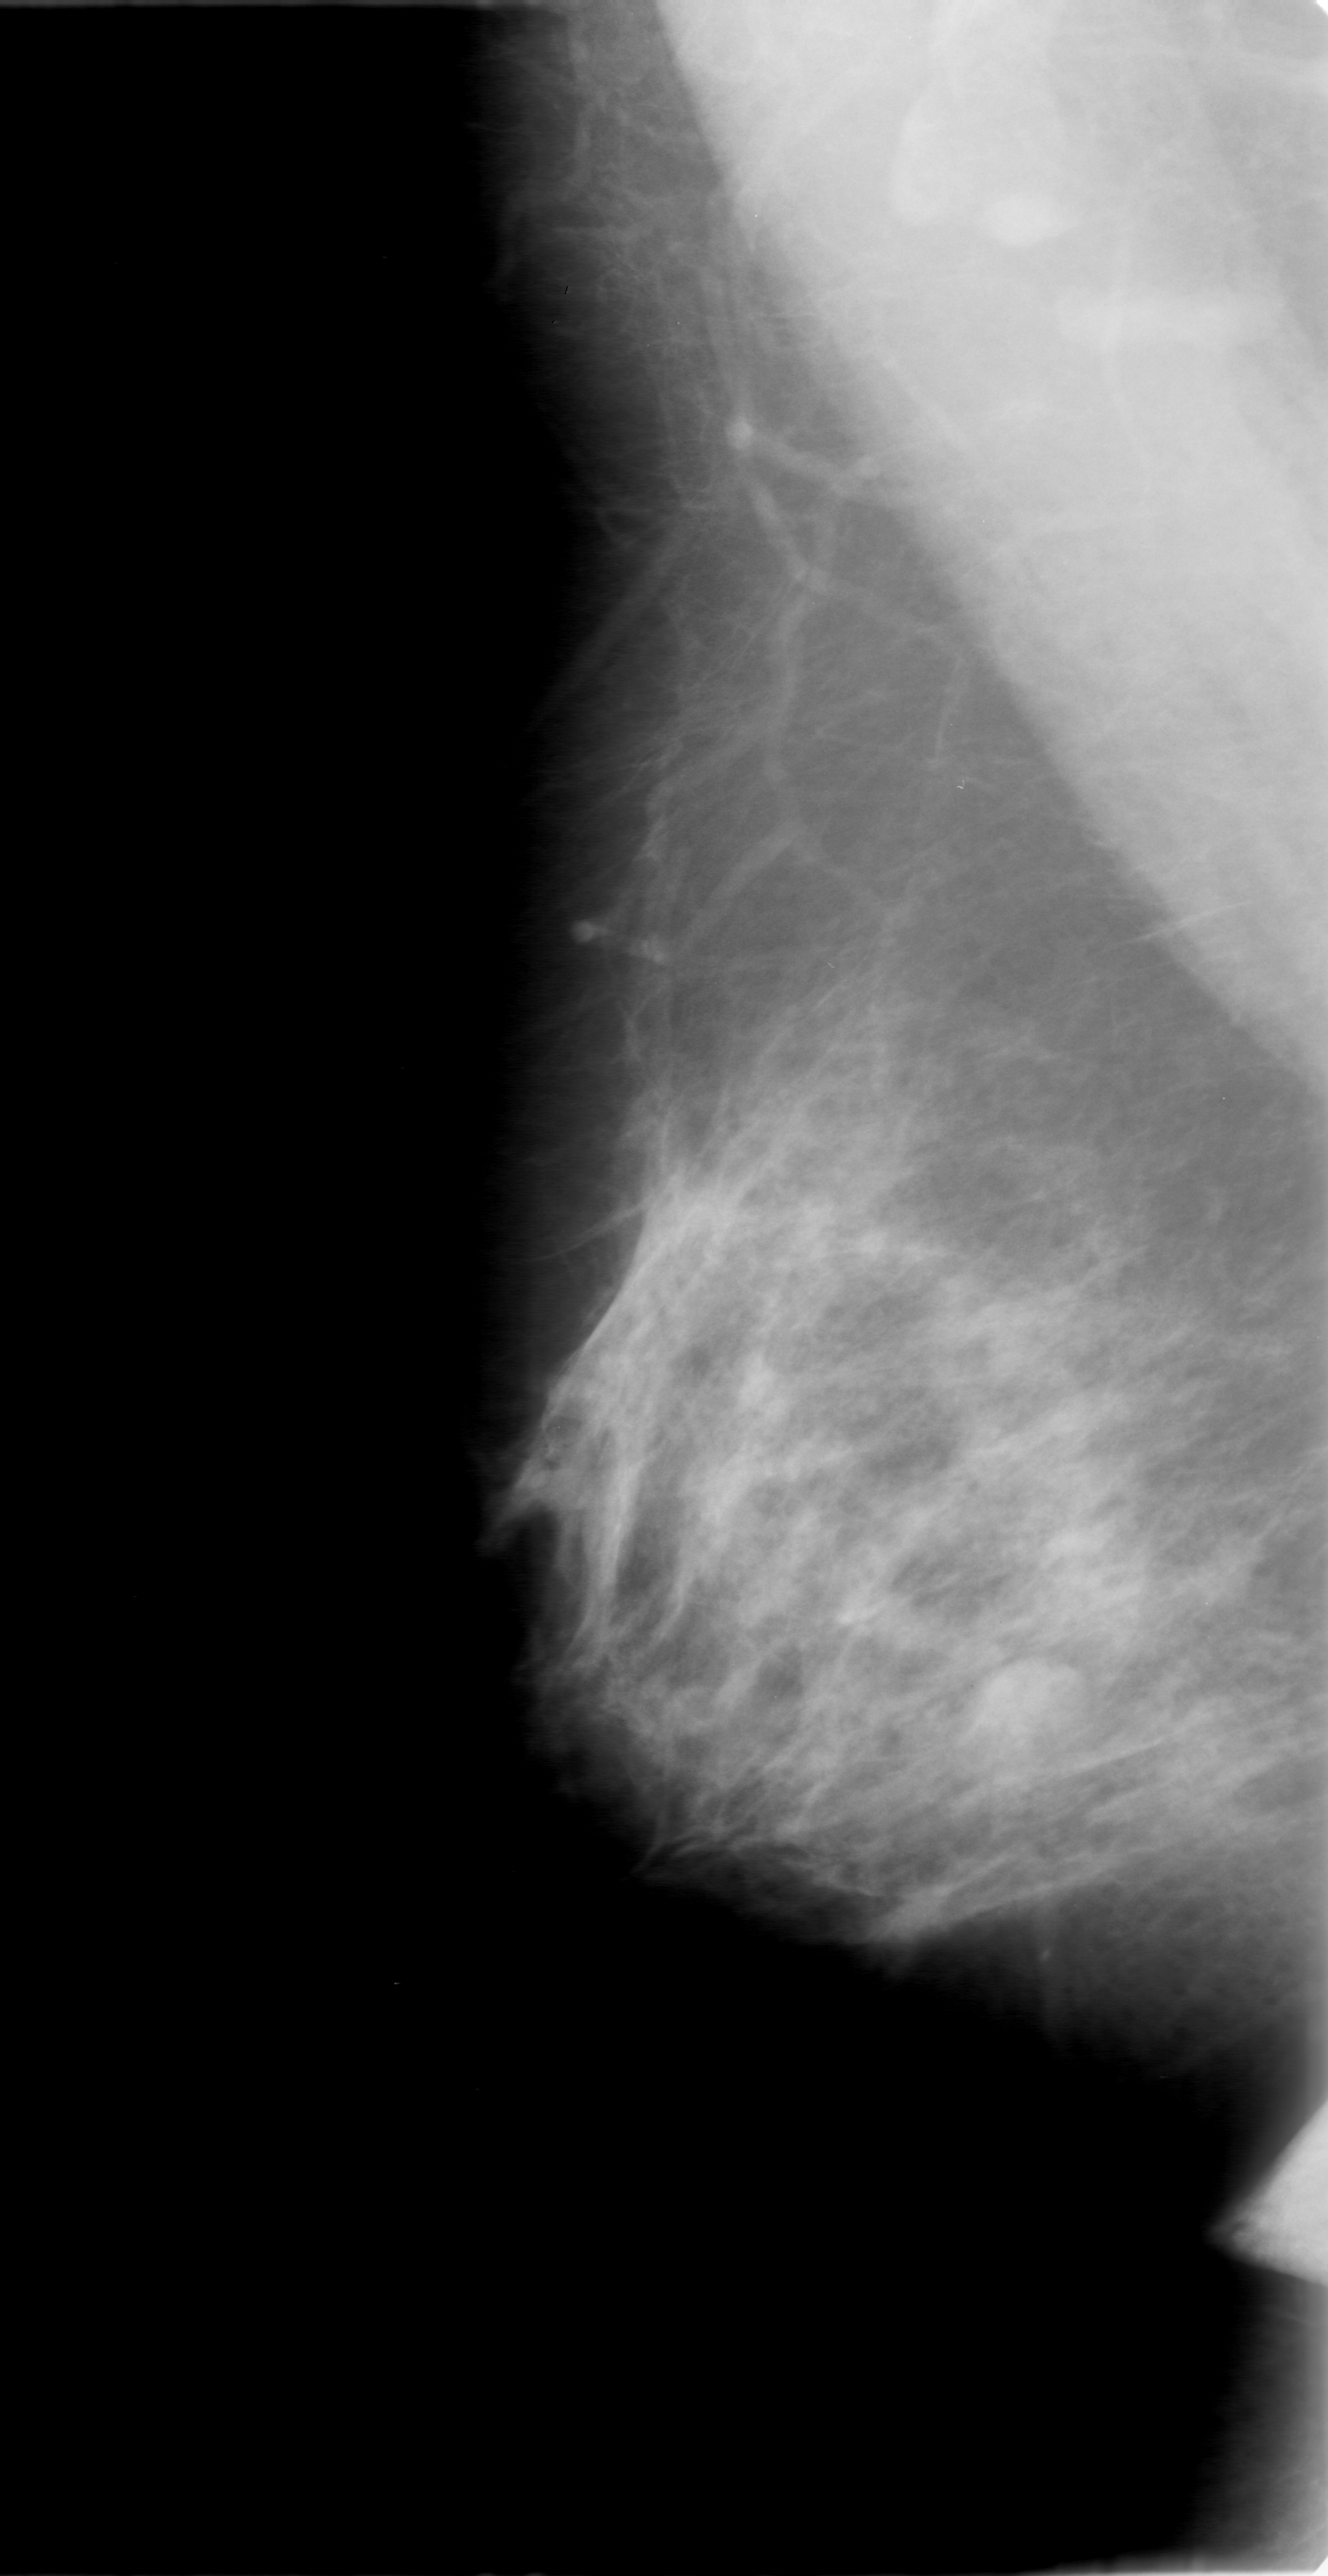
Mammogram (digitized film), right breast, mediolateral oblique (MLO) view.
Marked findings (only marked abnormalities are described; nothing is implied about the rest of the image): mass, shape oval, margins microlobulated; BI-RADS assessment category 0; subtlety rating 4 on a 1 (subtle) to 5 (obvious) scale; pathology (as recorded): benign.